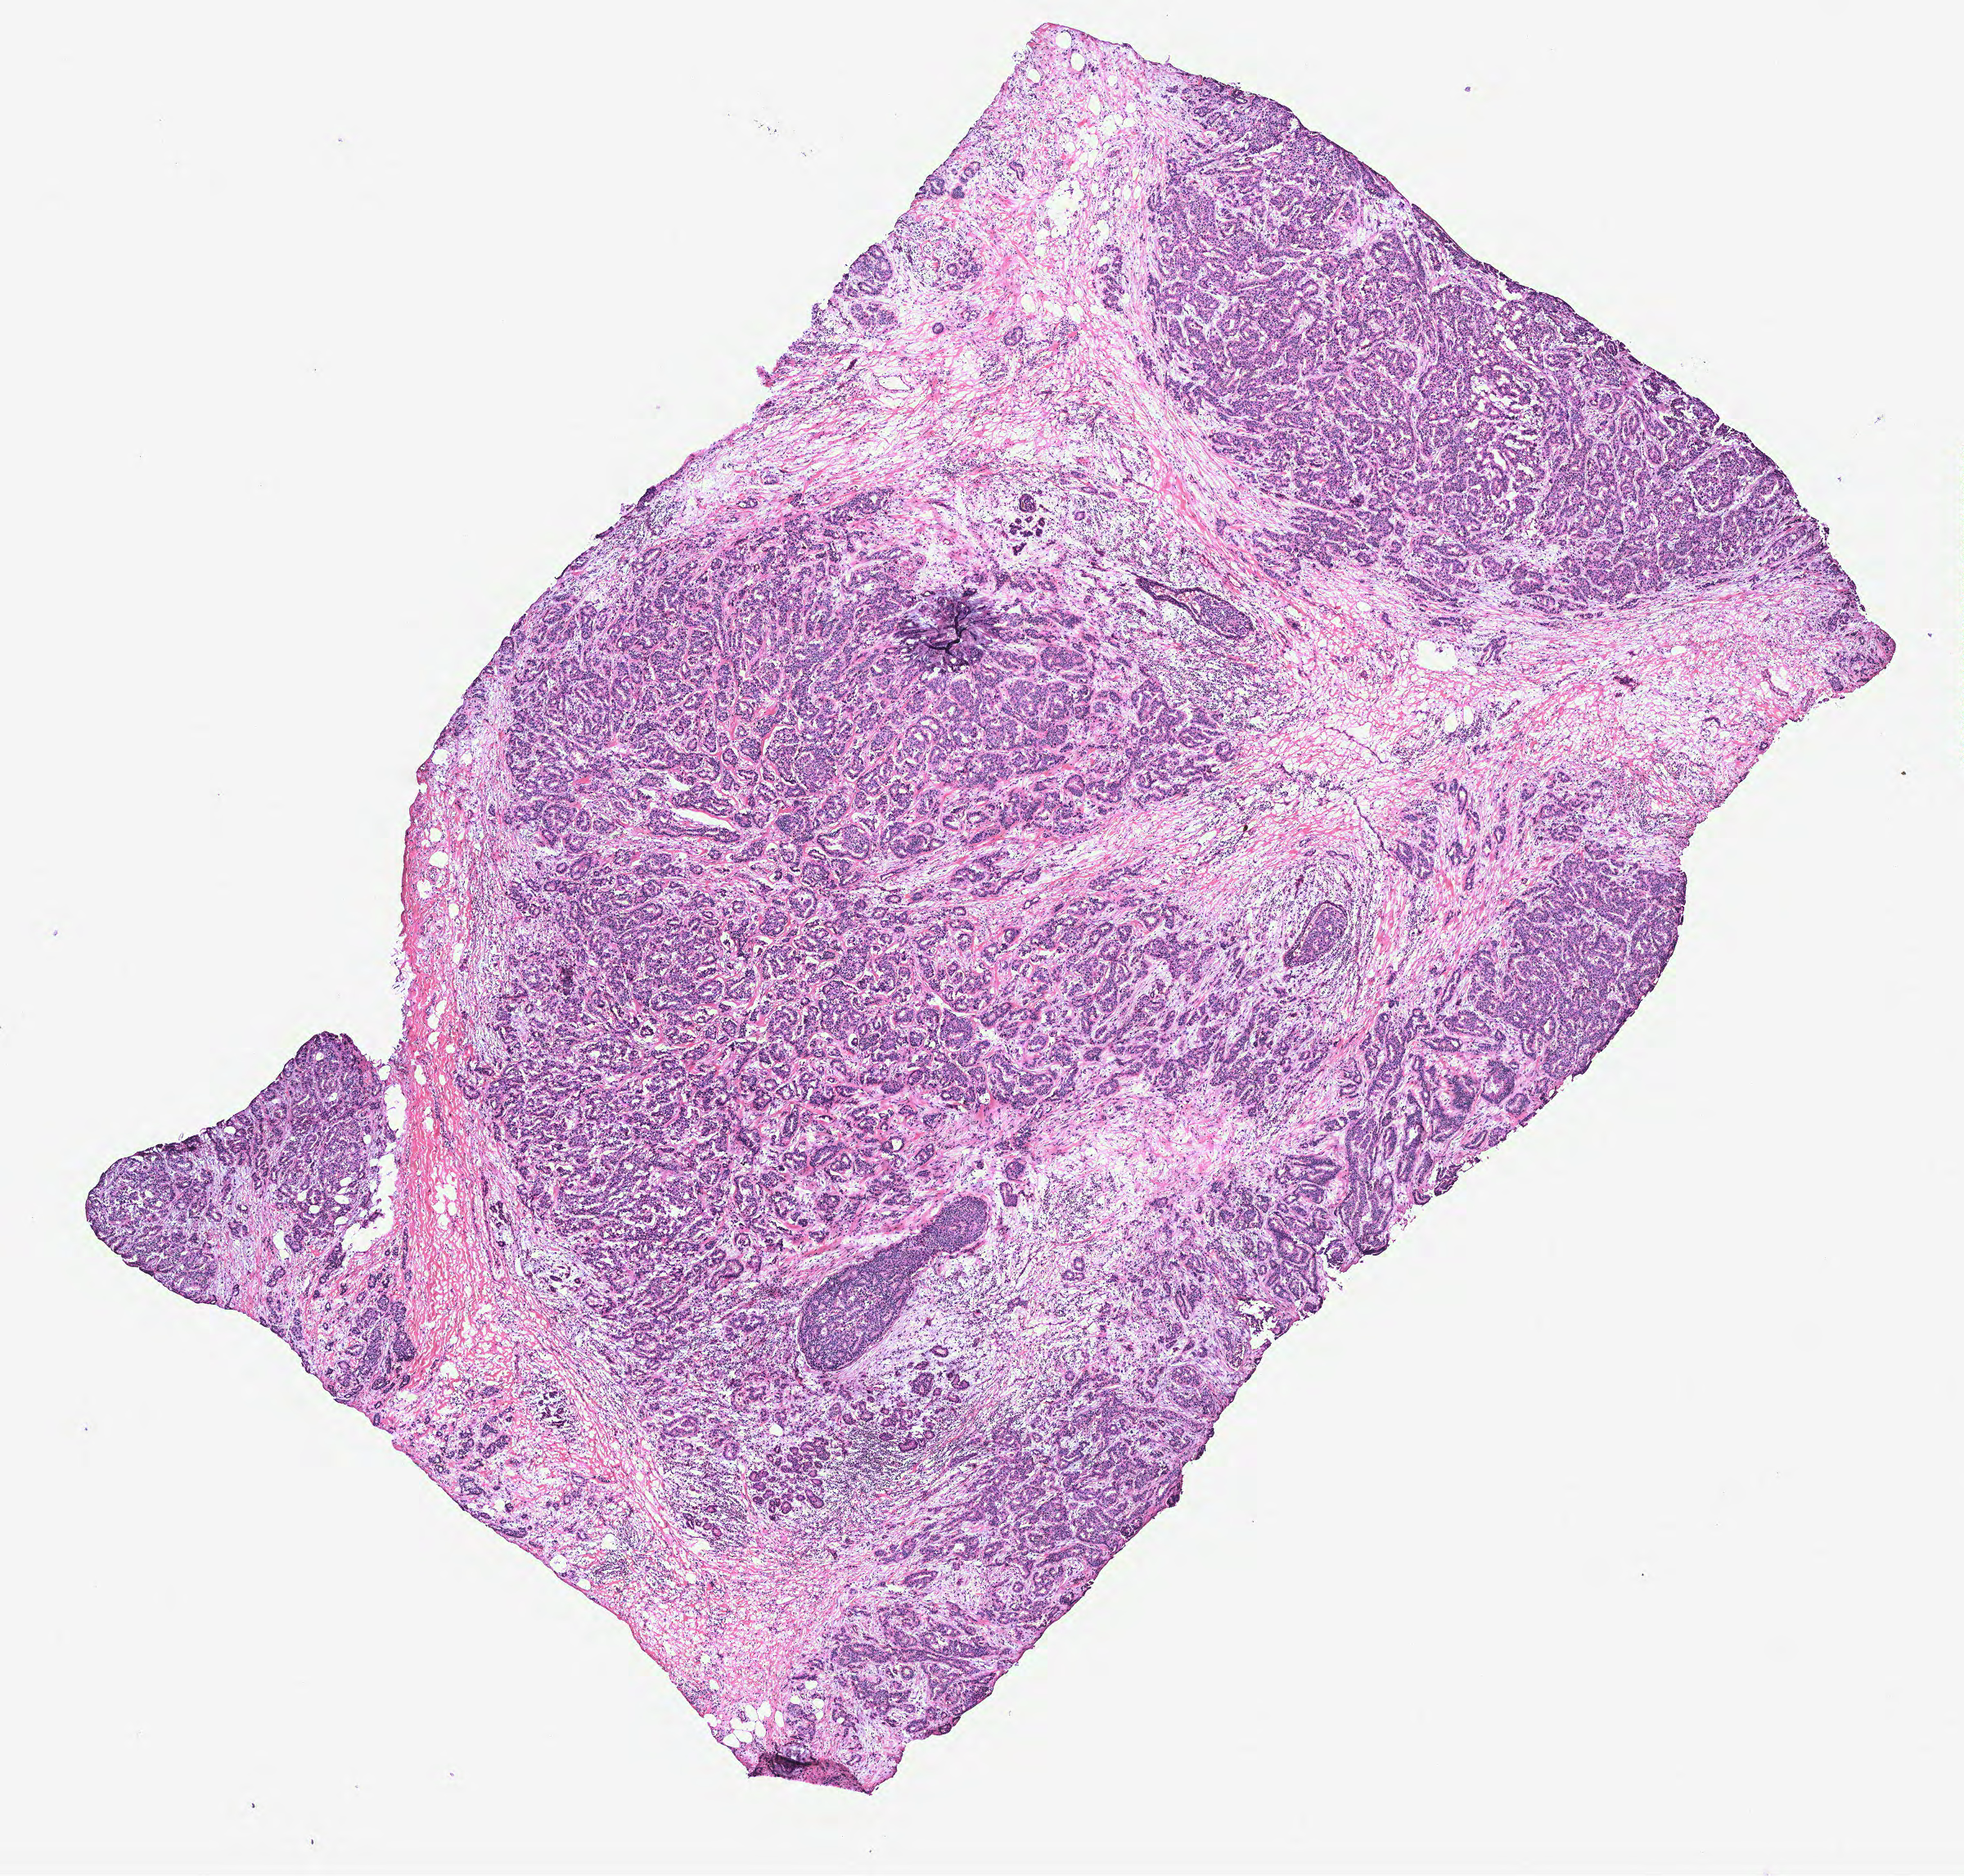
H&E whole-slide image — a low-resolution overview of the entire scanned area, about 9.6 x 9.2 mm (from a 40x scan); breast, tumour tissue. Patient: female, age 55 years.
• AJCC pathologic stage: IIIA
• diagnosis: Infiltrating duct carcinoma, NOS